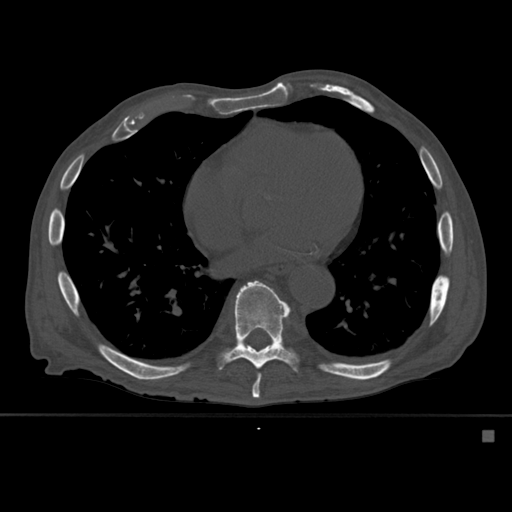
CT including the spine, one axial slice; slice 335 of 527 in the series (ordered by position); bone window (W 1800 / L 400 HU); 1.5 mm slice thickness; 512 × 512 image matrix, field of view 373 × 373 mm. Male patient, age 78 years. Case-level facts recorded for this patient, not image findings: primary cancer: prostate.
Structures marked on this image (semi-automatic segmentation, software-assisted and operator-edited):
- T8 vertebra: box from (x=252, y=374) to (x=261, y=399) px
- T9 vertebra: (x=219, y=280)–(x=298, y=390)